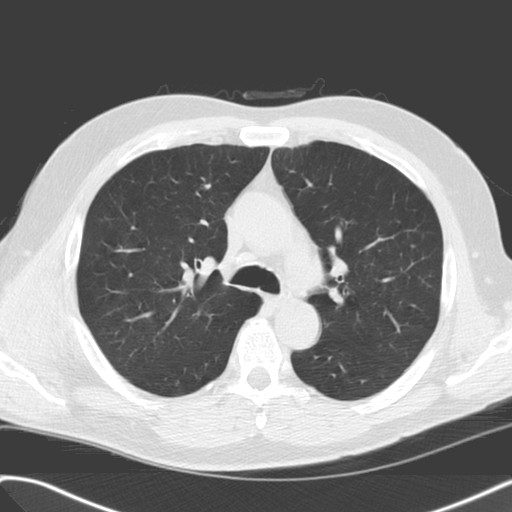
Low-dose screening chest CT, axial slice, baseline screening round, lung window (W 1500 / L -600 HU), 3.2 mm slice thickness, standard (soft-tissue) reconstruction kernel (C), slice 57 of 157 in the series, 512 × 512 image matrix, field of view 360 × 360 mm. Male, age 61 years at enrolment. Current smoker at enrolment.
• Lesion marked by an expert reader, bounding box <103,237,137,263> (left, top, right, bottom; pixels).
• The exam's reader record, not a measurement of the box and not confirmed to be the same lesion: non-calcified nodule or mass ≥4 mm, right upper lobe, 6 × 6 mm, smooth margins, soft tissue attenuation.
• Official screen result: positive, change unspecified: nodule(s) >= 4 mm or enlarging nodule(s), mass(es), or other non-specific abnormalities suspicious for lung cancer.
• Participant outcome: lung cancer diagnosed 746 days after this screen (after the third annual screen) — adenocarcinoma, NOS, right upper lobe, stage IIIA (AJCC 6th edition), 13 mm at pathology.